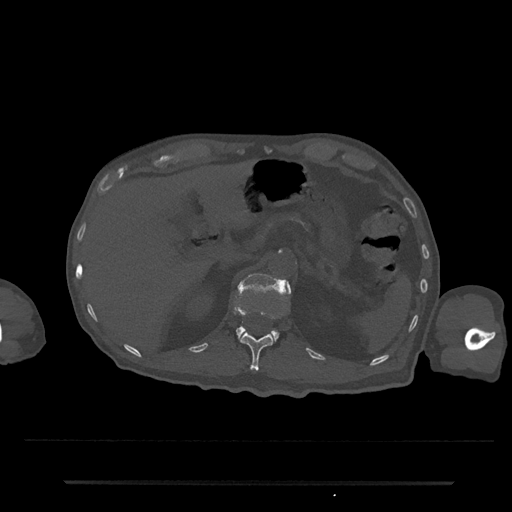
CT including the spine, one axial slice; slice 172 of 797 in the series (ordered by position); reconstruction kernel Br40s/3; bone window (W 1800 / L 400 HU); 0.5 mm slice thickness; 512 × 512 image matrix, field of view 427 × 427 mm. Male patient, age 74 years. Case-level facts recorded for this patient, not image findings: primary cancer: prostate.
Annotated regions visible in this slice (semi-automatic segmentation, software-assisted and operator-edited):
- L1 vertebra: bounding box <234,272,291,341> (left, top, right, bottom; pixels)
- T12 vertebra: <240,333,274,371>